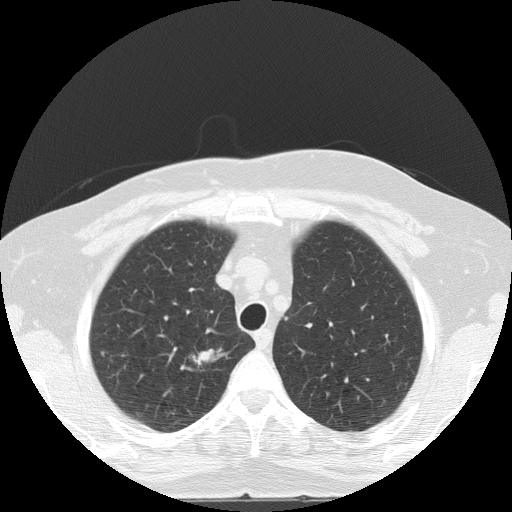
Low-dose screening chest CT, one axial slice. Slice 108 of 133 in the series (ordered by position). Reconstruction kernel FC51. Lung window (W 1500 / L -600 HU). 512 × 512 image matrix.
Annotated regions visible in this slice (expert manual segmentation):
- lesion 1 (tumor, upper lobe of right lung): bounding box (x1, y1, x2, y2) in pixels: (191, 348, 227, 367)